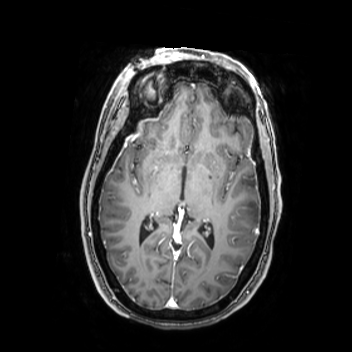
Brain MRI from a brain-tumour surgery series, one axial slice; position 145 of 350 along the scan axis; T1-weighted post-contrast; 0.9 mm slice thickness; 352 × 352 image matrix, field of view 280 × 280 mm. From the clinical record (not read from this slice): histopathology: Oligodendroglioma; WHO grade: 2; IDH mutation: yes.
Outlined on this slice (expert manual segmentation):
- tumour: bounding box <224,182,262,224> (left, top, right, bottom; pixels)